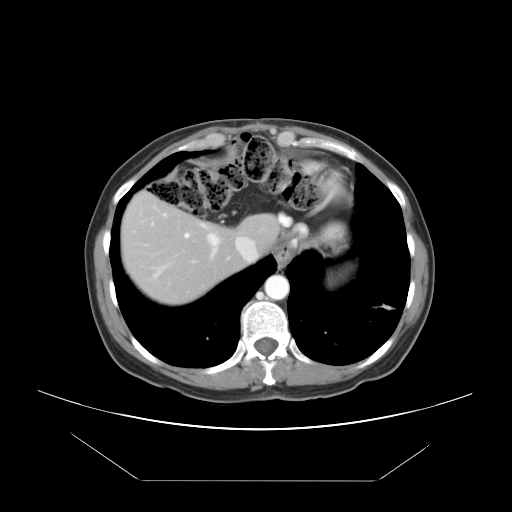
Contrast-enhanced abdominal CT, one axial slice; position 38 of 45 along the scan axis; reconstruction kernel STANDARD; 120 kVp; intravenous contrast given; soft-tissue window (W 400 / L 40 HU); 5 mm slice thickness; 512 × 512 image matrix, field of view 405 × 405 mm. Female patient, age 52 years. Case-level facts recorded for this patient, not image findings: diagnosis: colorectal cancer liver metastases, imaged before liver resection; multiple liver metastases: yes; largest metastasis: 2.5 cm.
Annotated regions visible in this slice (manually delineated by an expert):
- hepatic veins: box from (x=152, y=212) to (x=256, y=280) px
- liver: (x=123, y=196)–(x=276, y=302)
- planned liver remnant (the part of the liver to remain after resection): (x=123, y=196)–(x=275, y=287)
- portal vein (with intrahepatic branches): (x=184, y=233)–(x=190, y=239)